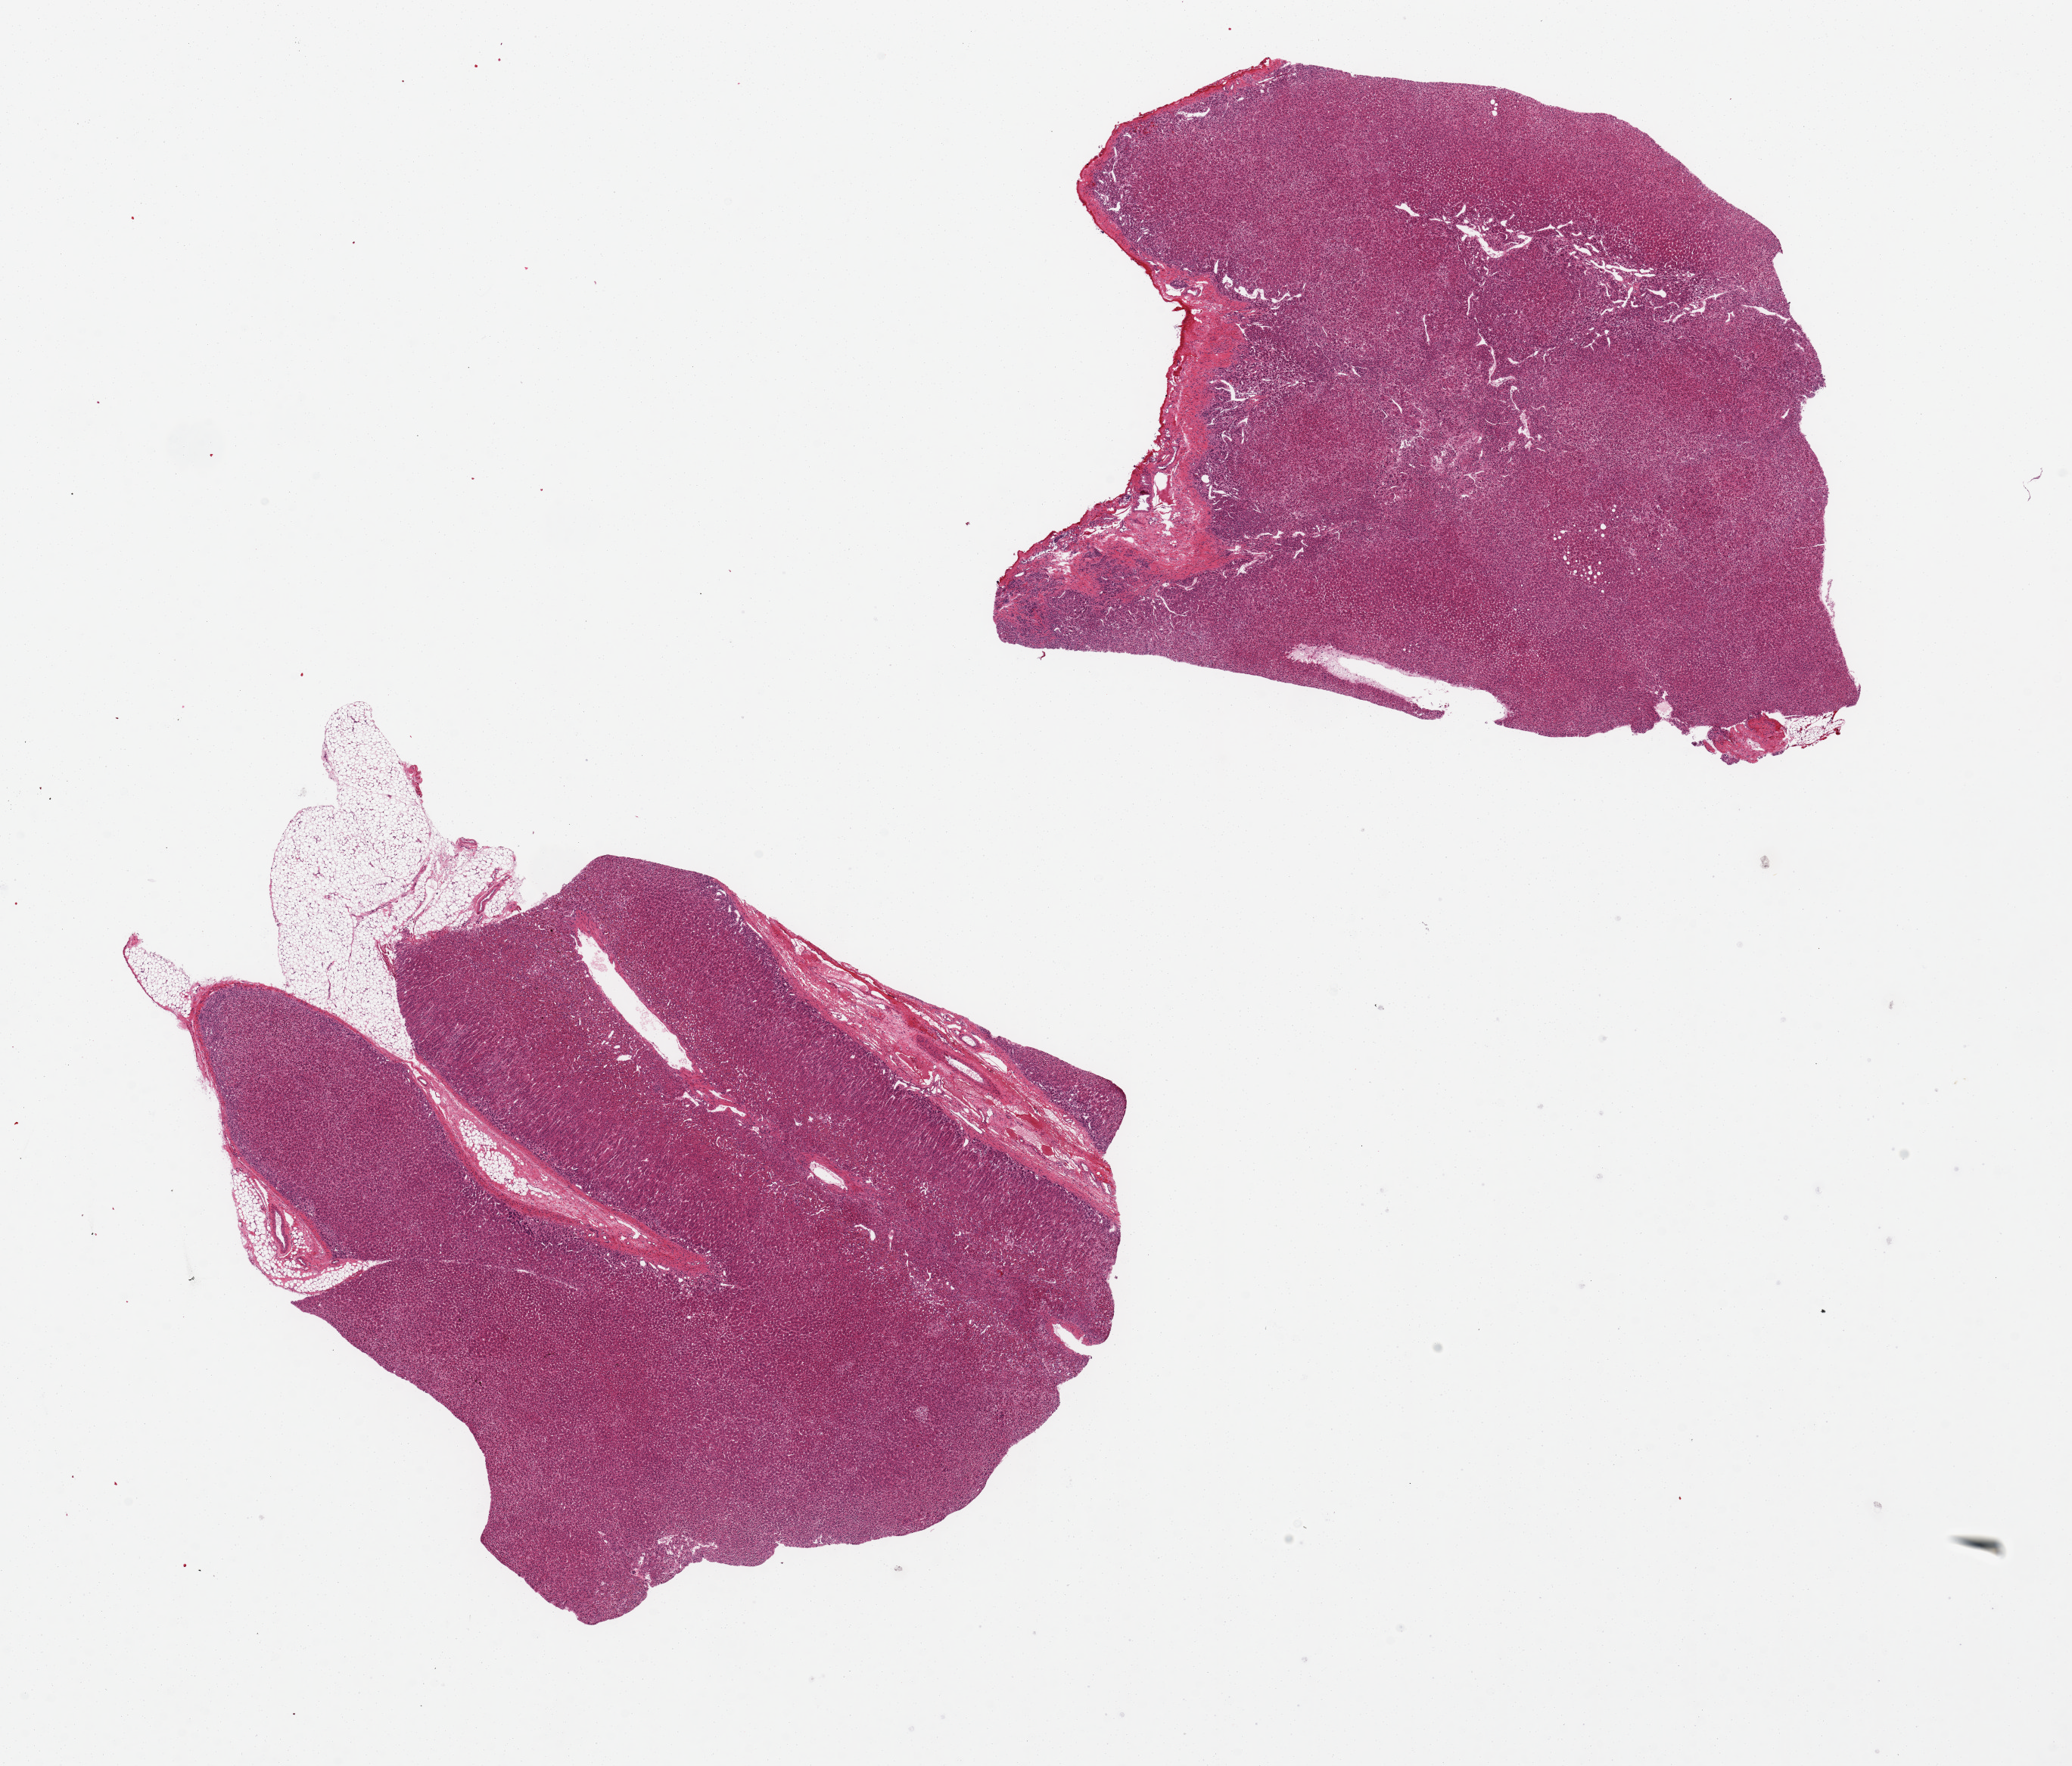
Digitized hematoxylin and eosin (H&E)-stained section, whole scanned area (about 21.7 x 18.5 mm, acquisition: 20x scan) shown as a low-resolution overview, PAXgene-fixed paraffin-embedded (PFPE) section, section of adrenal gland (target tissue), tissue donor sample. Donor: male.
* reviewer comment on this tissue sample: 2 aliquots, 7x6mm. All cortex, well-preserved